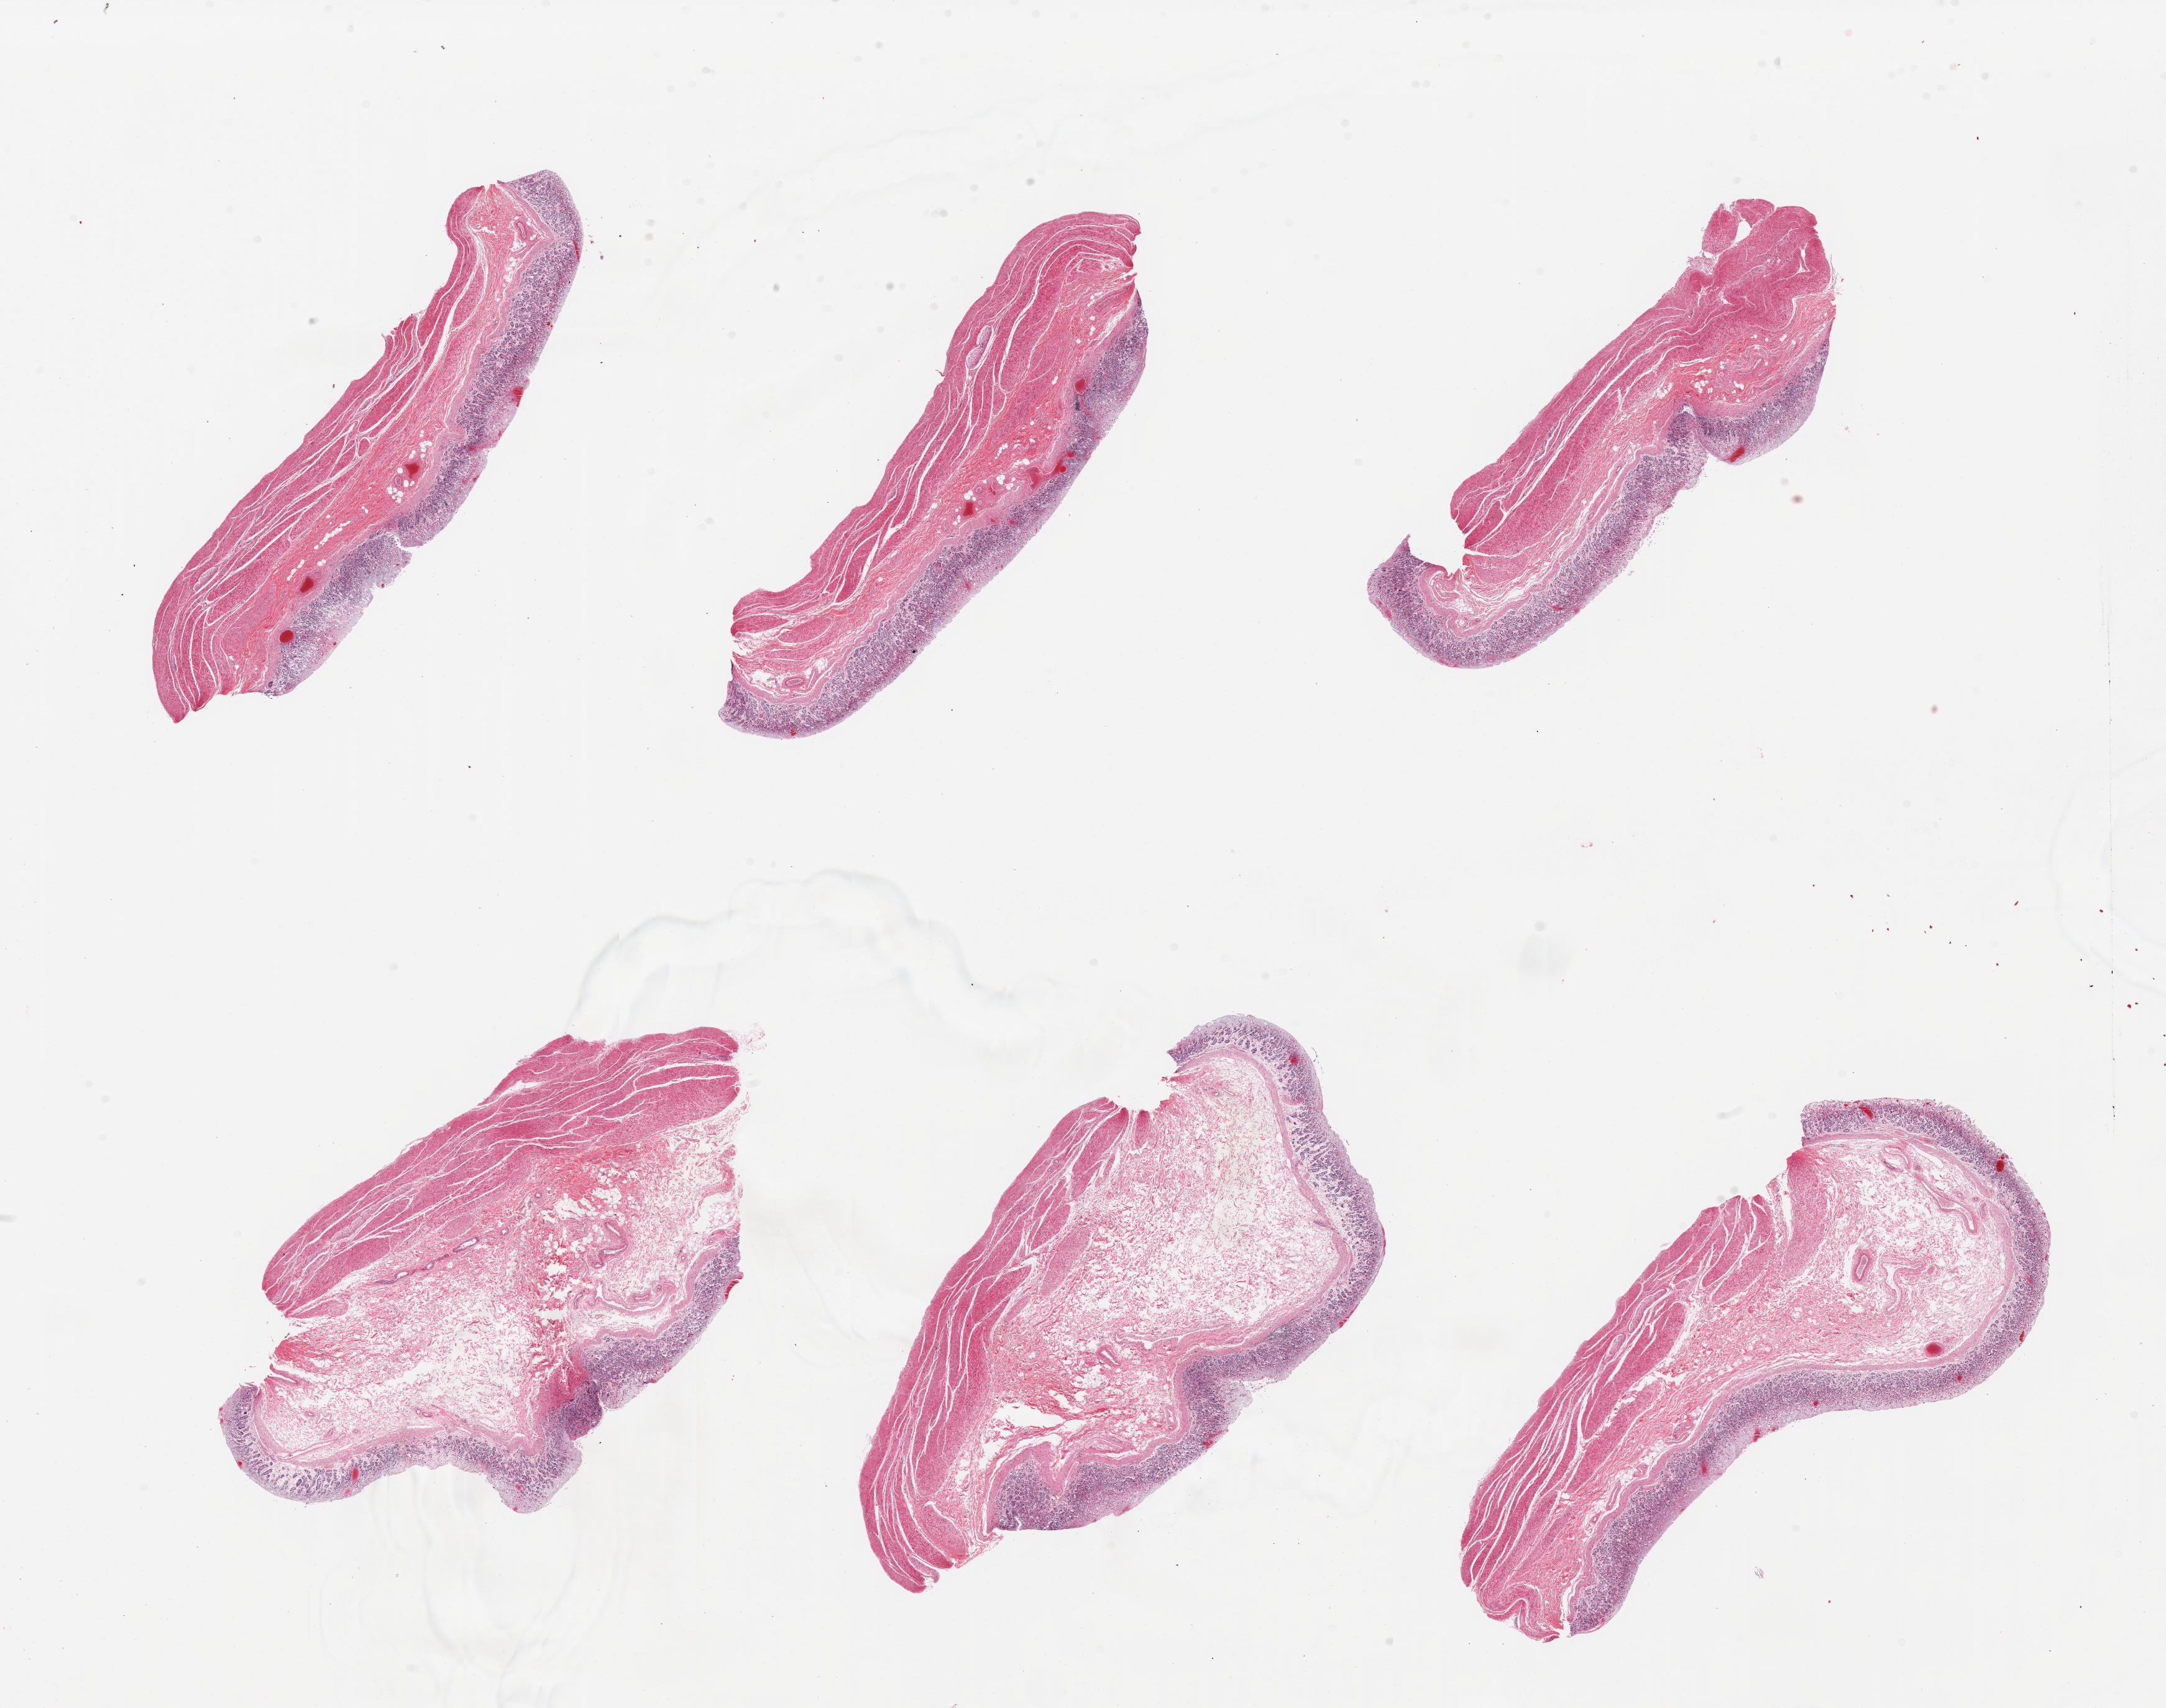
Digitized H&E-stained section — a low-resolution overview of the entire scanned area, about 27.6 x 21.7 mm, PAXgene-fixed, paraffin-embedded tissue, sampled site (target tissue): stomach, tissue donor sample. Donor sex: male.
Review note (as recorded): 6 pieces; full thickness sections, moderate autolysis.